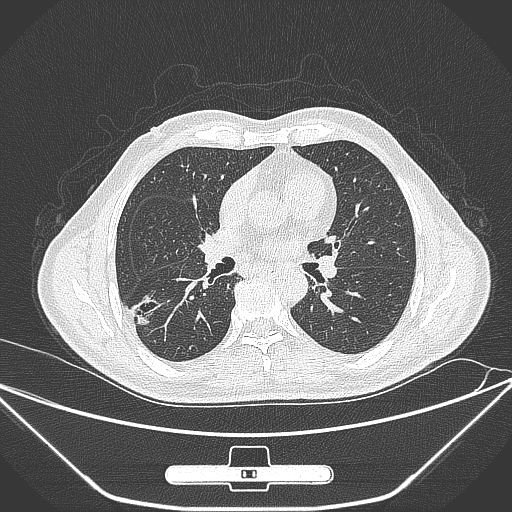
Chest CT, one axial slice. 120 kVp. Lung window (W 1500 / L -600 HU). 1 mm slice thickness. 512 × 512 image matrix, field of view 398 × 398 mm. Patient: male, 71 years. From the clinical record (not read from this slice): clinical TNM (as recorded): T1c N0 M0.
Structures marked on this image (bounding box drawn by a radiologist):
- lung tumour (recorded histology: adenocarcinoma): bounding box [x1, y1, x2, y2] px = [128, 294, 162, 331]